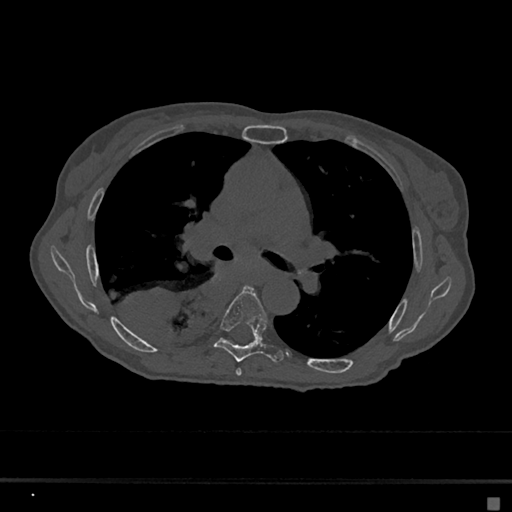
CT including the spine, one axial slice; reconstruction kernel Br40s/3; bone window (W 1800 / L 400 HU); 0.5 mm slice thickness; 512 × 512 image matrix, field of view 360 × 360 mm. Female patient, age 68 years. From the clinical record (not read from this slice): primary cancer: renal.
Annotated regions visible in this slice (semi-automatically segmented with operator editing):
- T5 vertebra: bounding box [x1, y1, x2, y2] px = [236, 369, 242, 376]
- T6 vertebra: [214, 286, 283, 363]